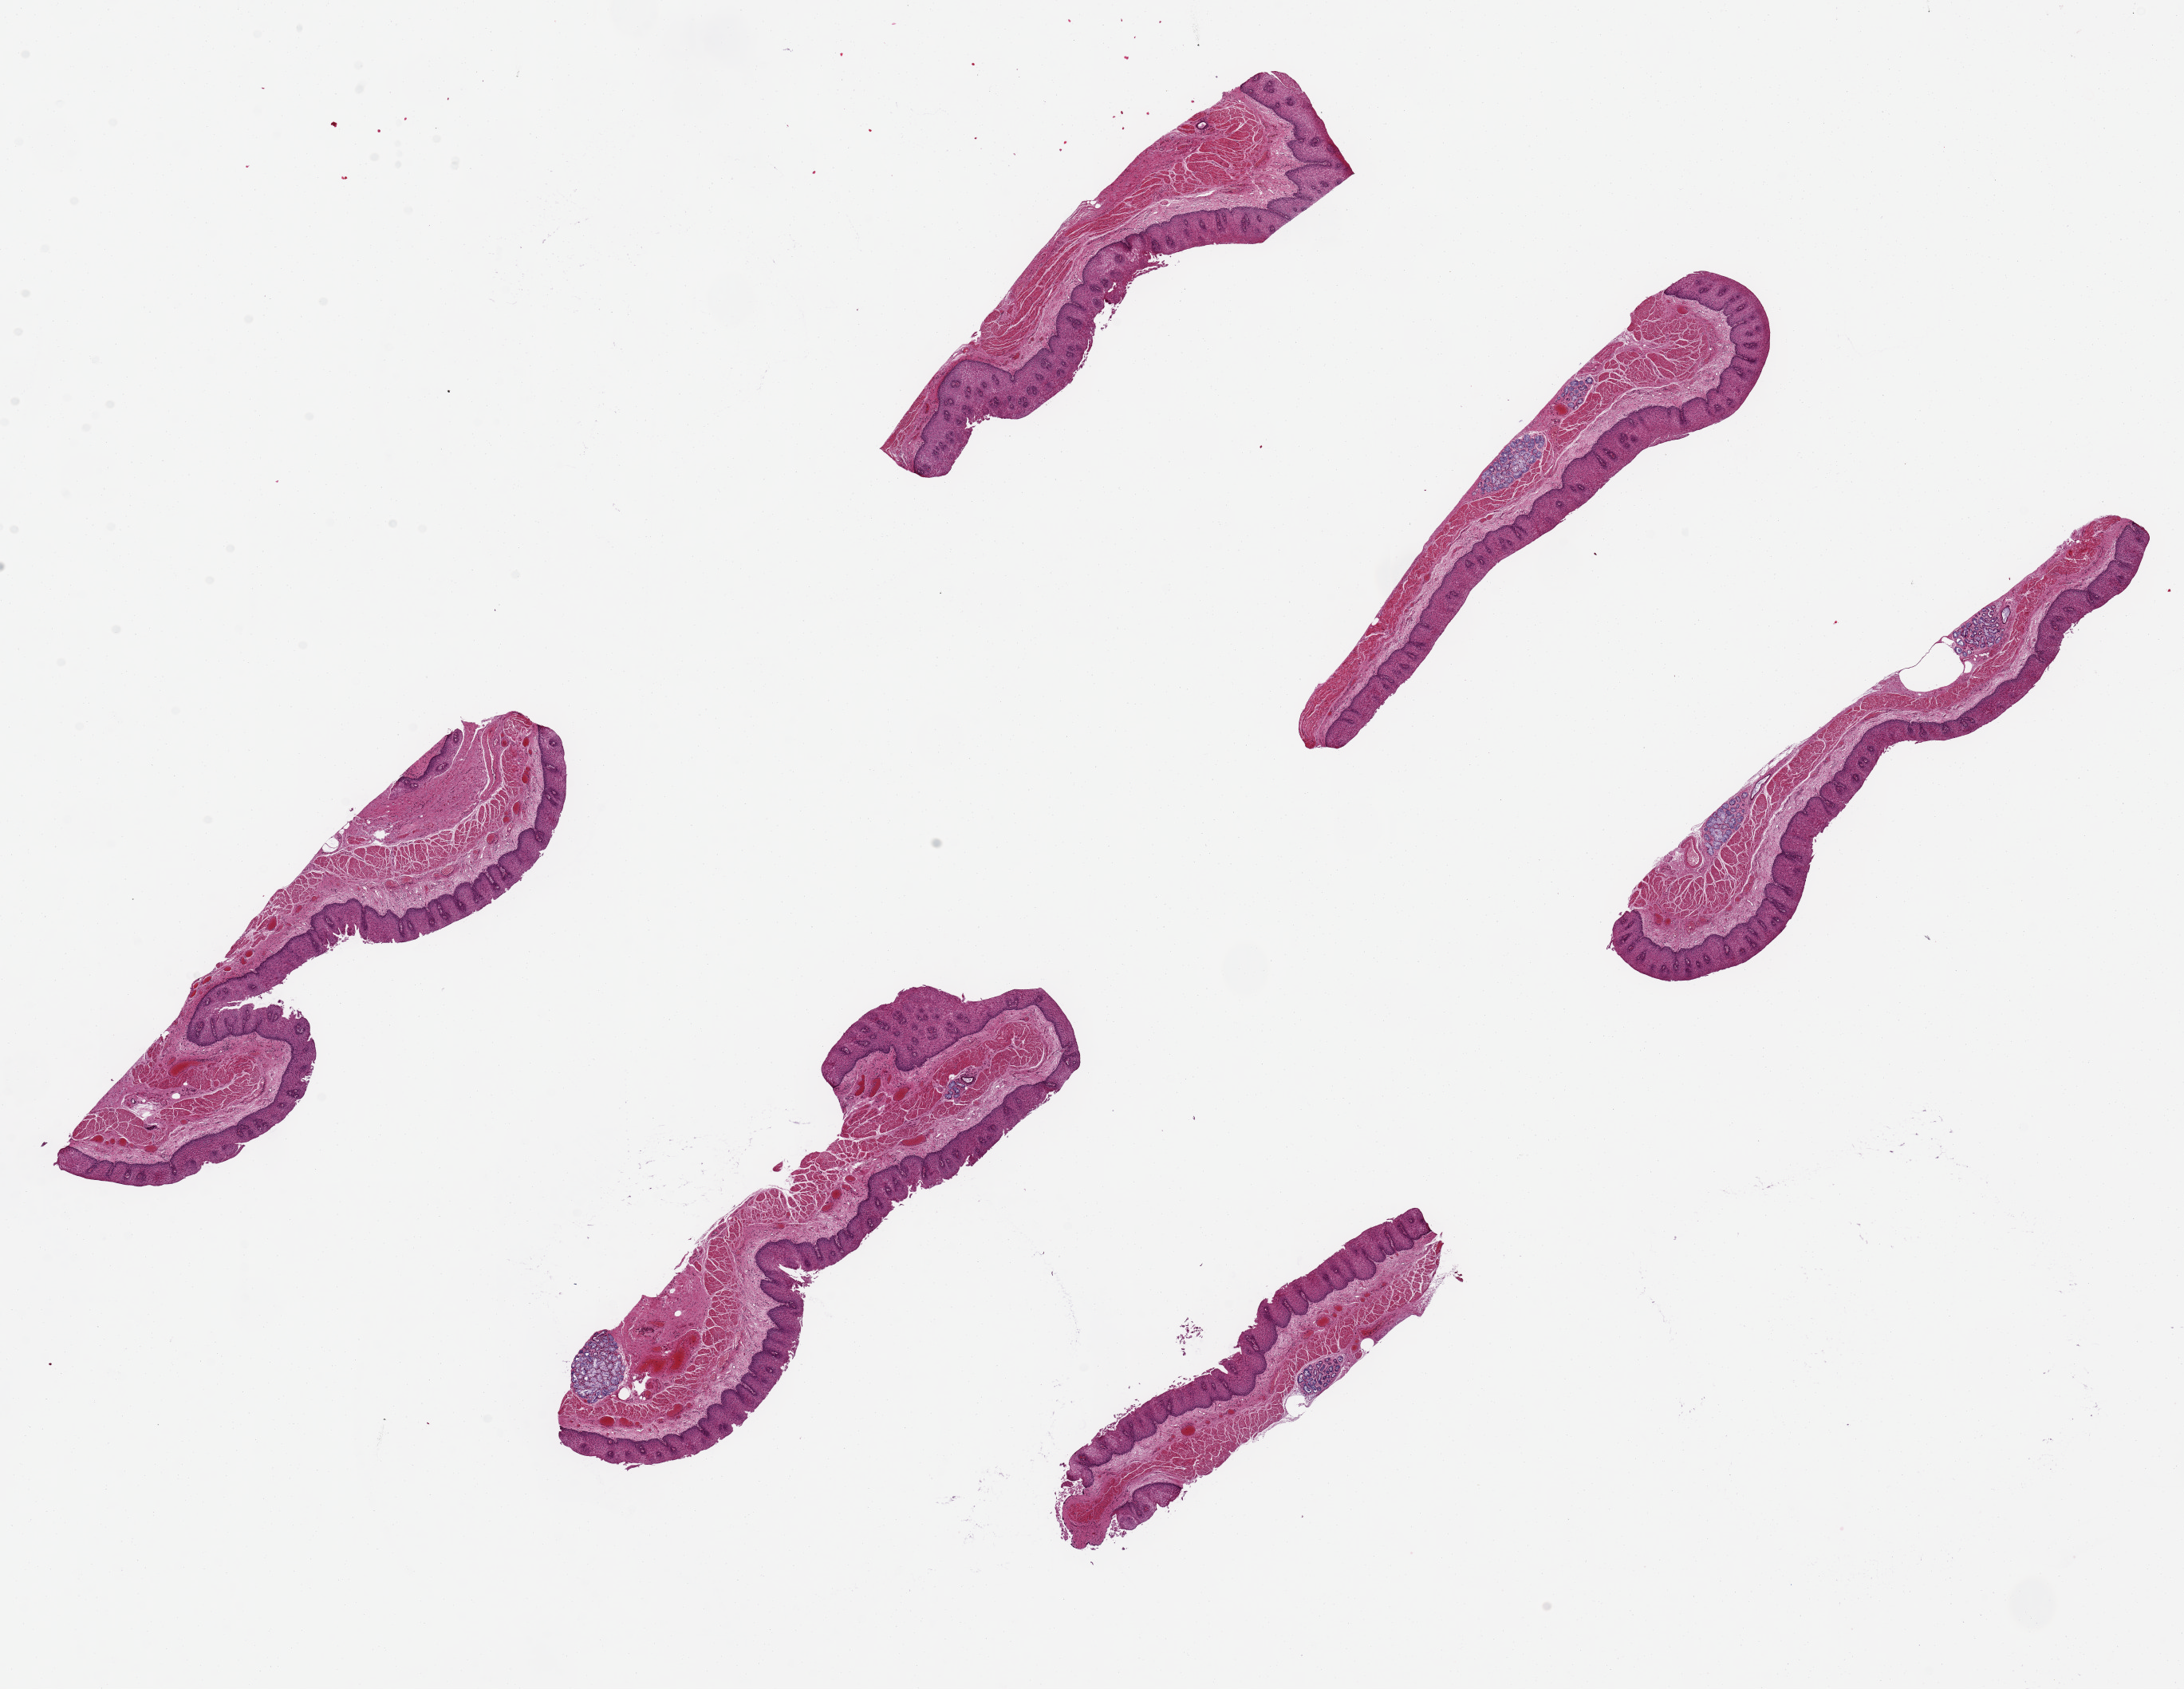
Hematoxylin and eosin (H&E) whole-slide image, a low-resolution overview of the entire scanned area, about 21.7 x 16.7 mm (from a 20x scan). PAXgene-fixed paraffin-embedded (PFPE) section. Target tissue: esophageal mucous membrane. Donor tissue sample.
Pathologist's review note for this sample: 6 pieces up to 6.5x1.4 mm; well preserved squamous mucosa and submucosal glands.